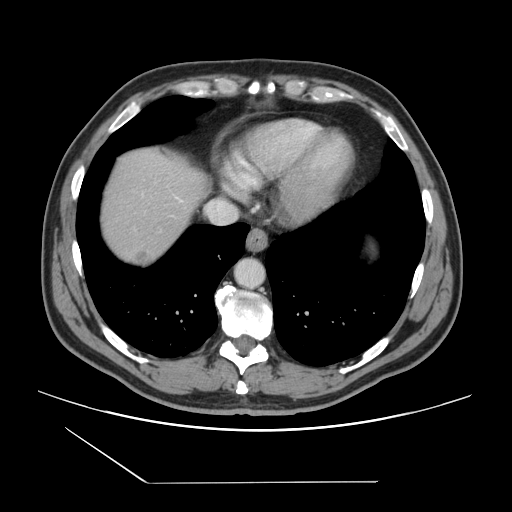
Contrast-enhanced abdominal CT, one axial slice; slice 133 of 157 in the series (ordered by position); intravenous contrast given; soft-tissue window (W 400 / L 40 HU); 512 × 512 image matrix, field of view 407 × 407 mm. Male patient, age 61 years. From the clinical record (not read from this slice): diagnosis: colorectal cancer liver metastases, imaged before liver resection.
Outlined on this slice (expert manual segmentation):
- liver: box from (x=101, y=152) to (x=207, y=266) px
- planned liver remnant (the part of the liver to remain after resection): (x=101, y=151)–(x=207, y=232)
- liver metastasis: (x=134, y=251)–(x=153, y=263)